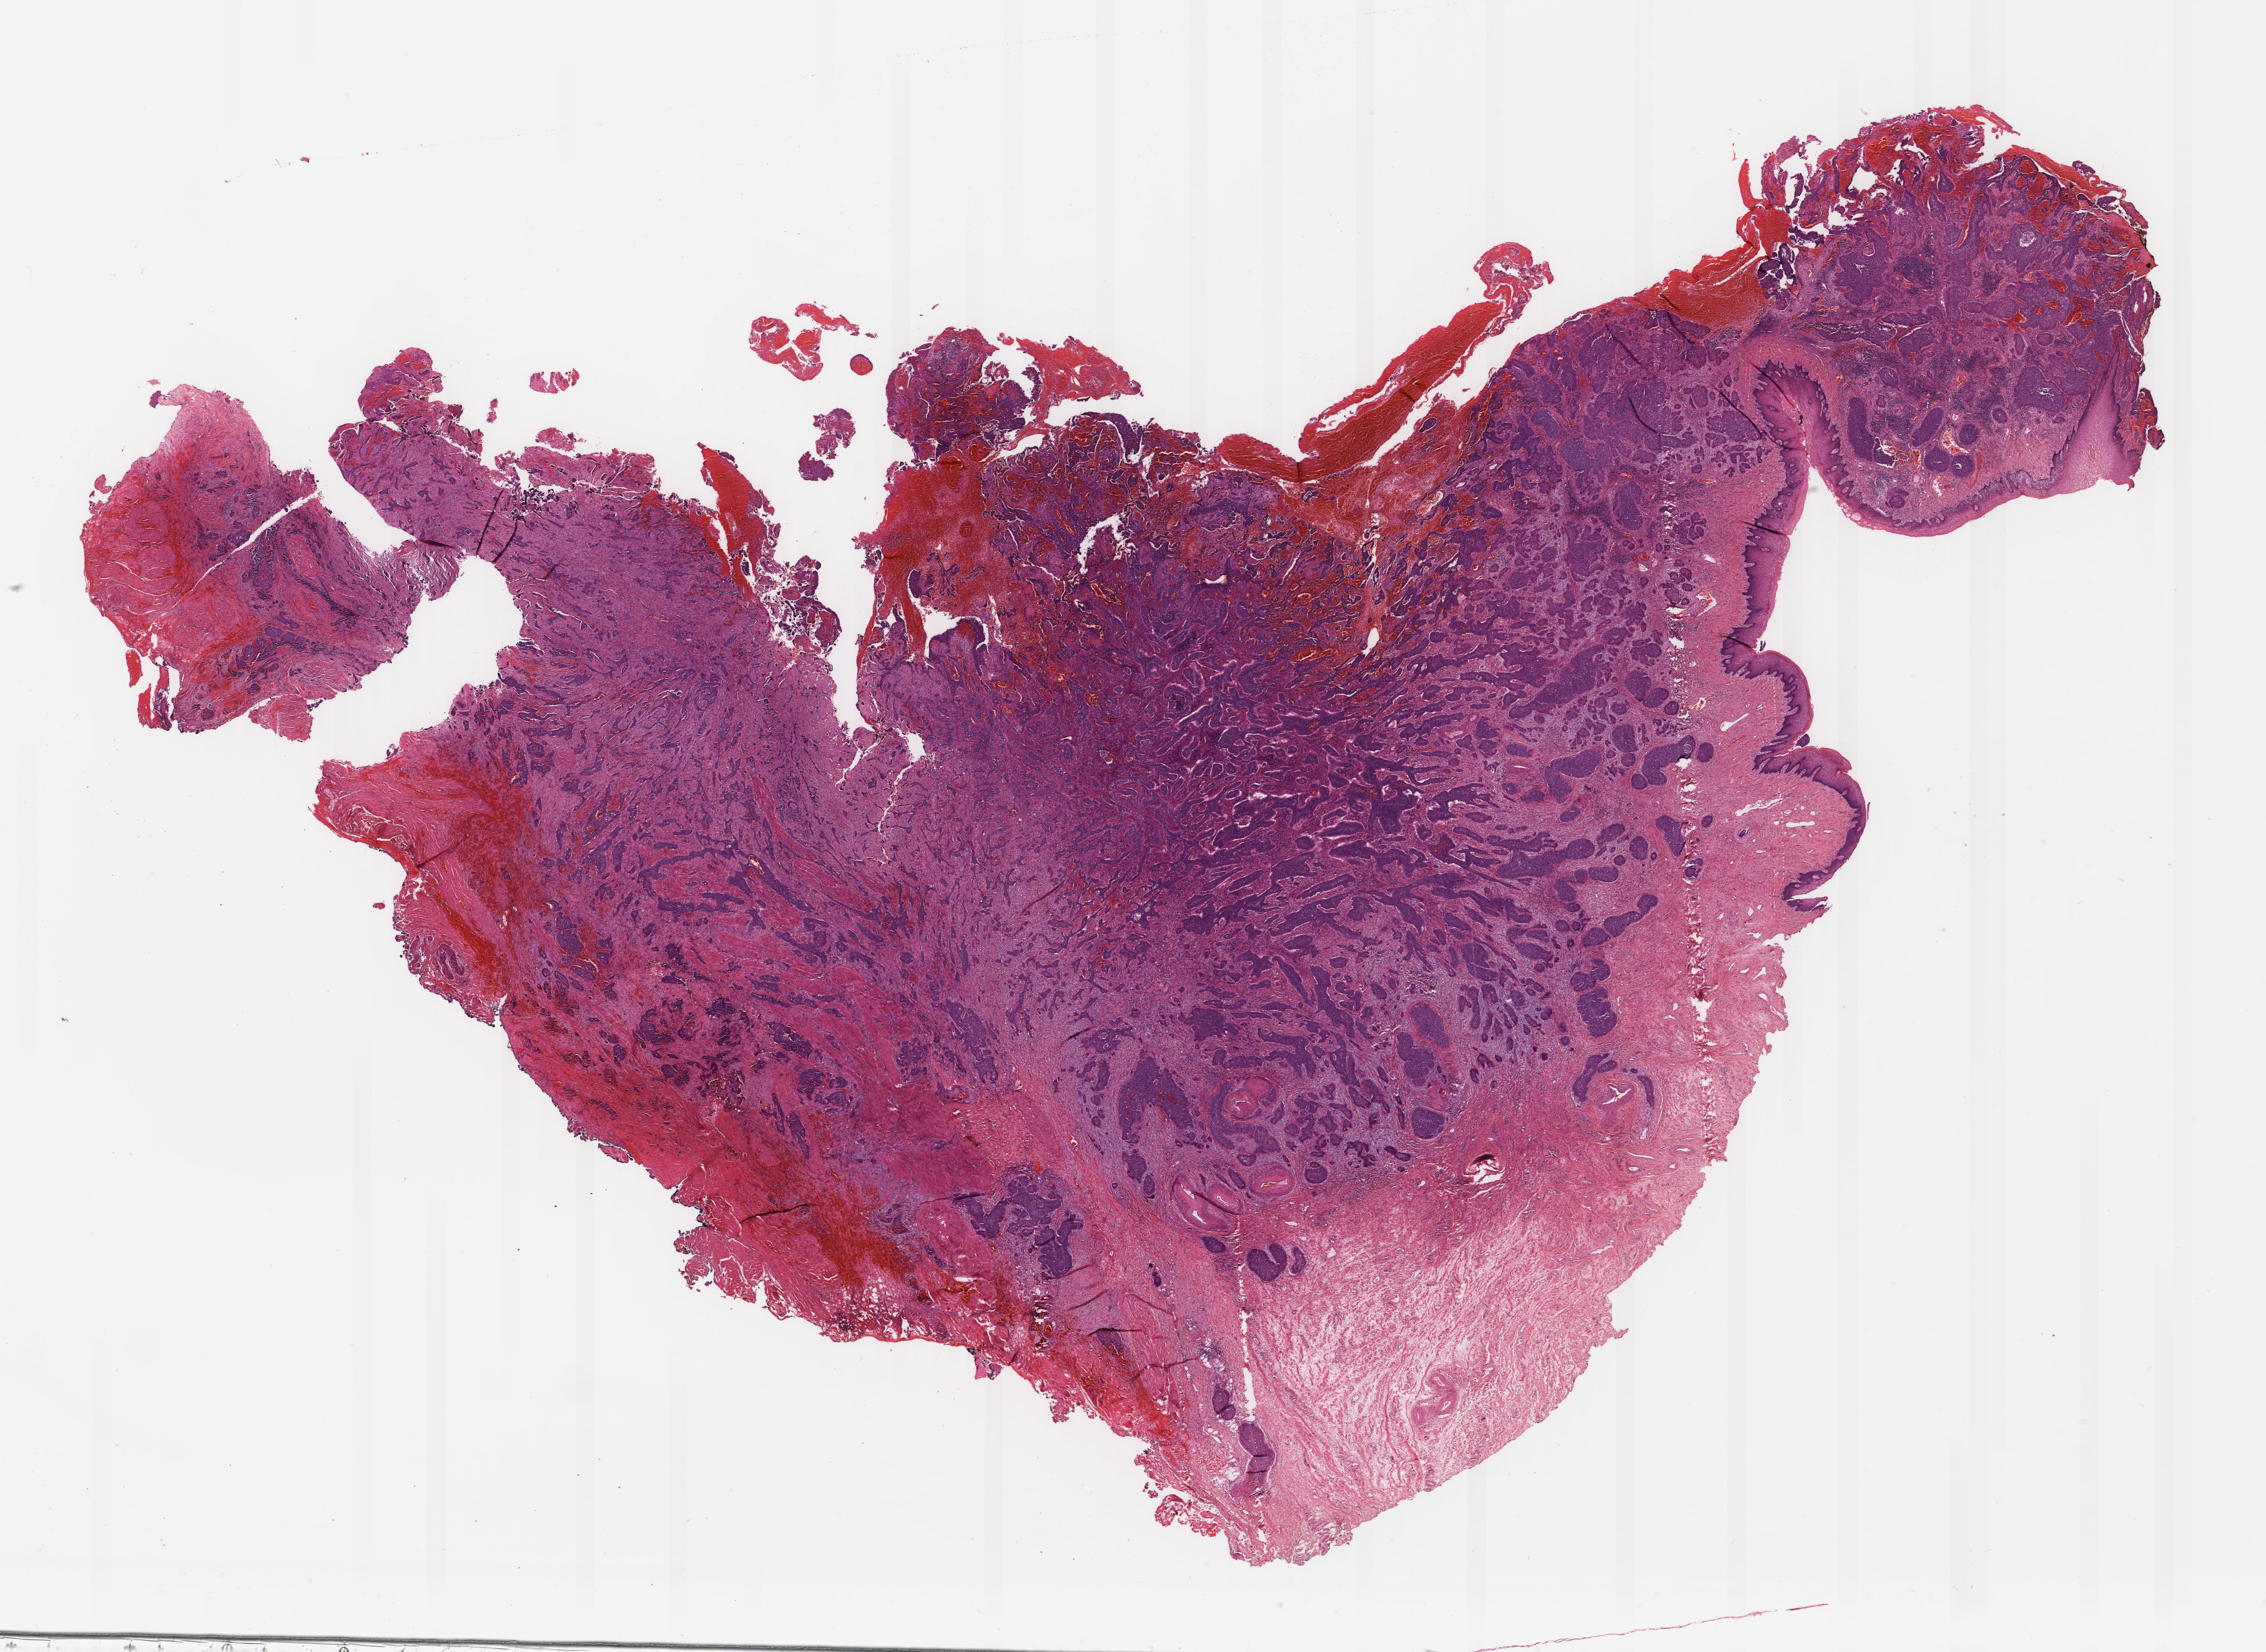
Whole-slide histology image, H&E-stained — low-resolution overview of the scanned area, about 28.8 x 21.0 mm (acquisition: 40x scan). Formalin-fixed paraffin-embedded (FFPE) diagnostic section. Sample: primary tumour, cervix. Patient: female, age at initial diagnosis 45 years. Histologic grade: G3 (poorly differentiated).
- histologic diagnosis: Squamous cell carcinoma, NOS (cervix uteri)
- lymph nodes positive (case pathology): 1 of 16 examined